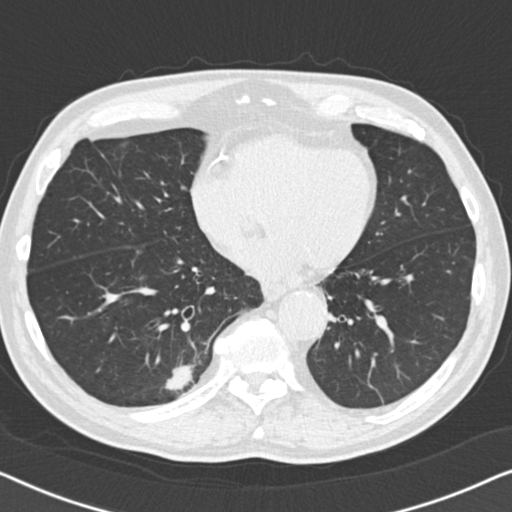
Axial slice from a low-dose chest CT screening exam. Second annual screen. Lung window (W 1500 / L -600 HU). Standard (soft-tissue) reconstruction kernel (B30f). Slice 113 of 164 in the series. 512 × 512 image matrix, field of view 330 × 330 mm. Male participant, aged 74 years at enrolment. Current smoker at enrolment.
Expert reader's lesion annotation, bounding box [x1, y1, x2, y2] px = [150, 346, 218, 406]. The screening reader recorded 5 non-calcified nodules or masses ≥4 mm on this exam; which of them this box marks is not recorded. Lung cancer was diagnosed 55 days after this screen: bronchiolo-alveolar adenocarcinoma, NOS, right lower lobe, moderately differentiated (G2), stage IA (AJCC 6th edition), 16 mm at pathology.